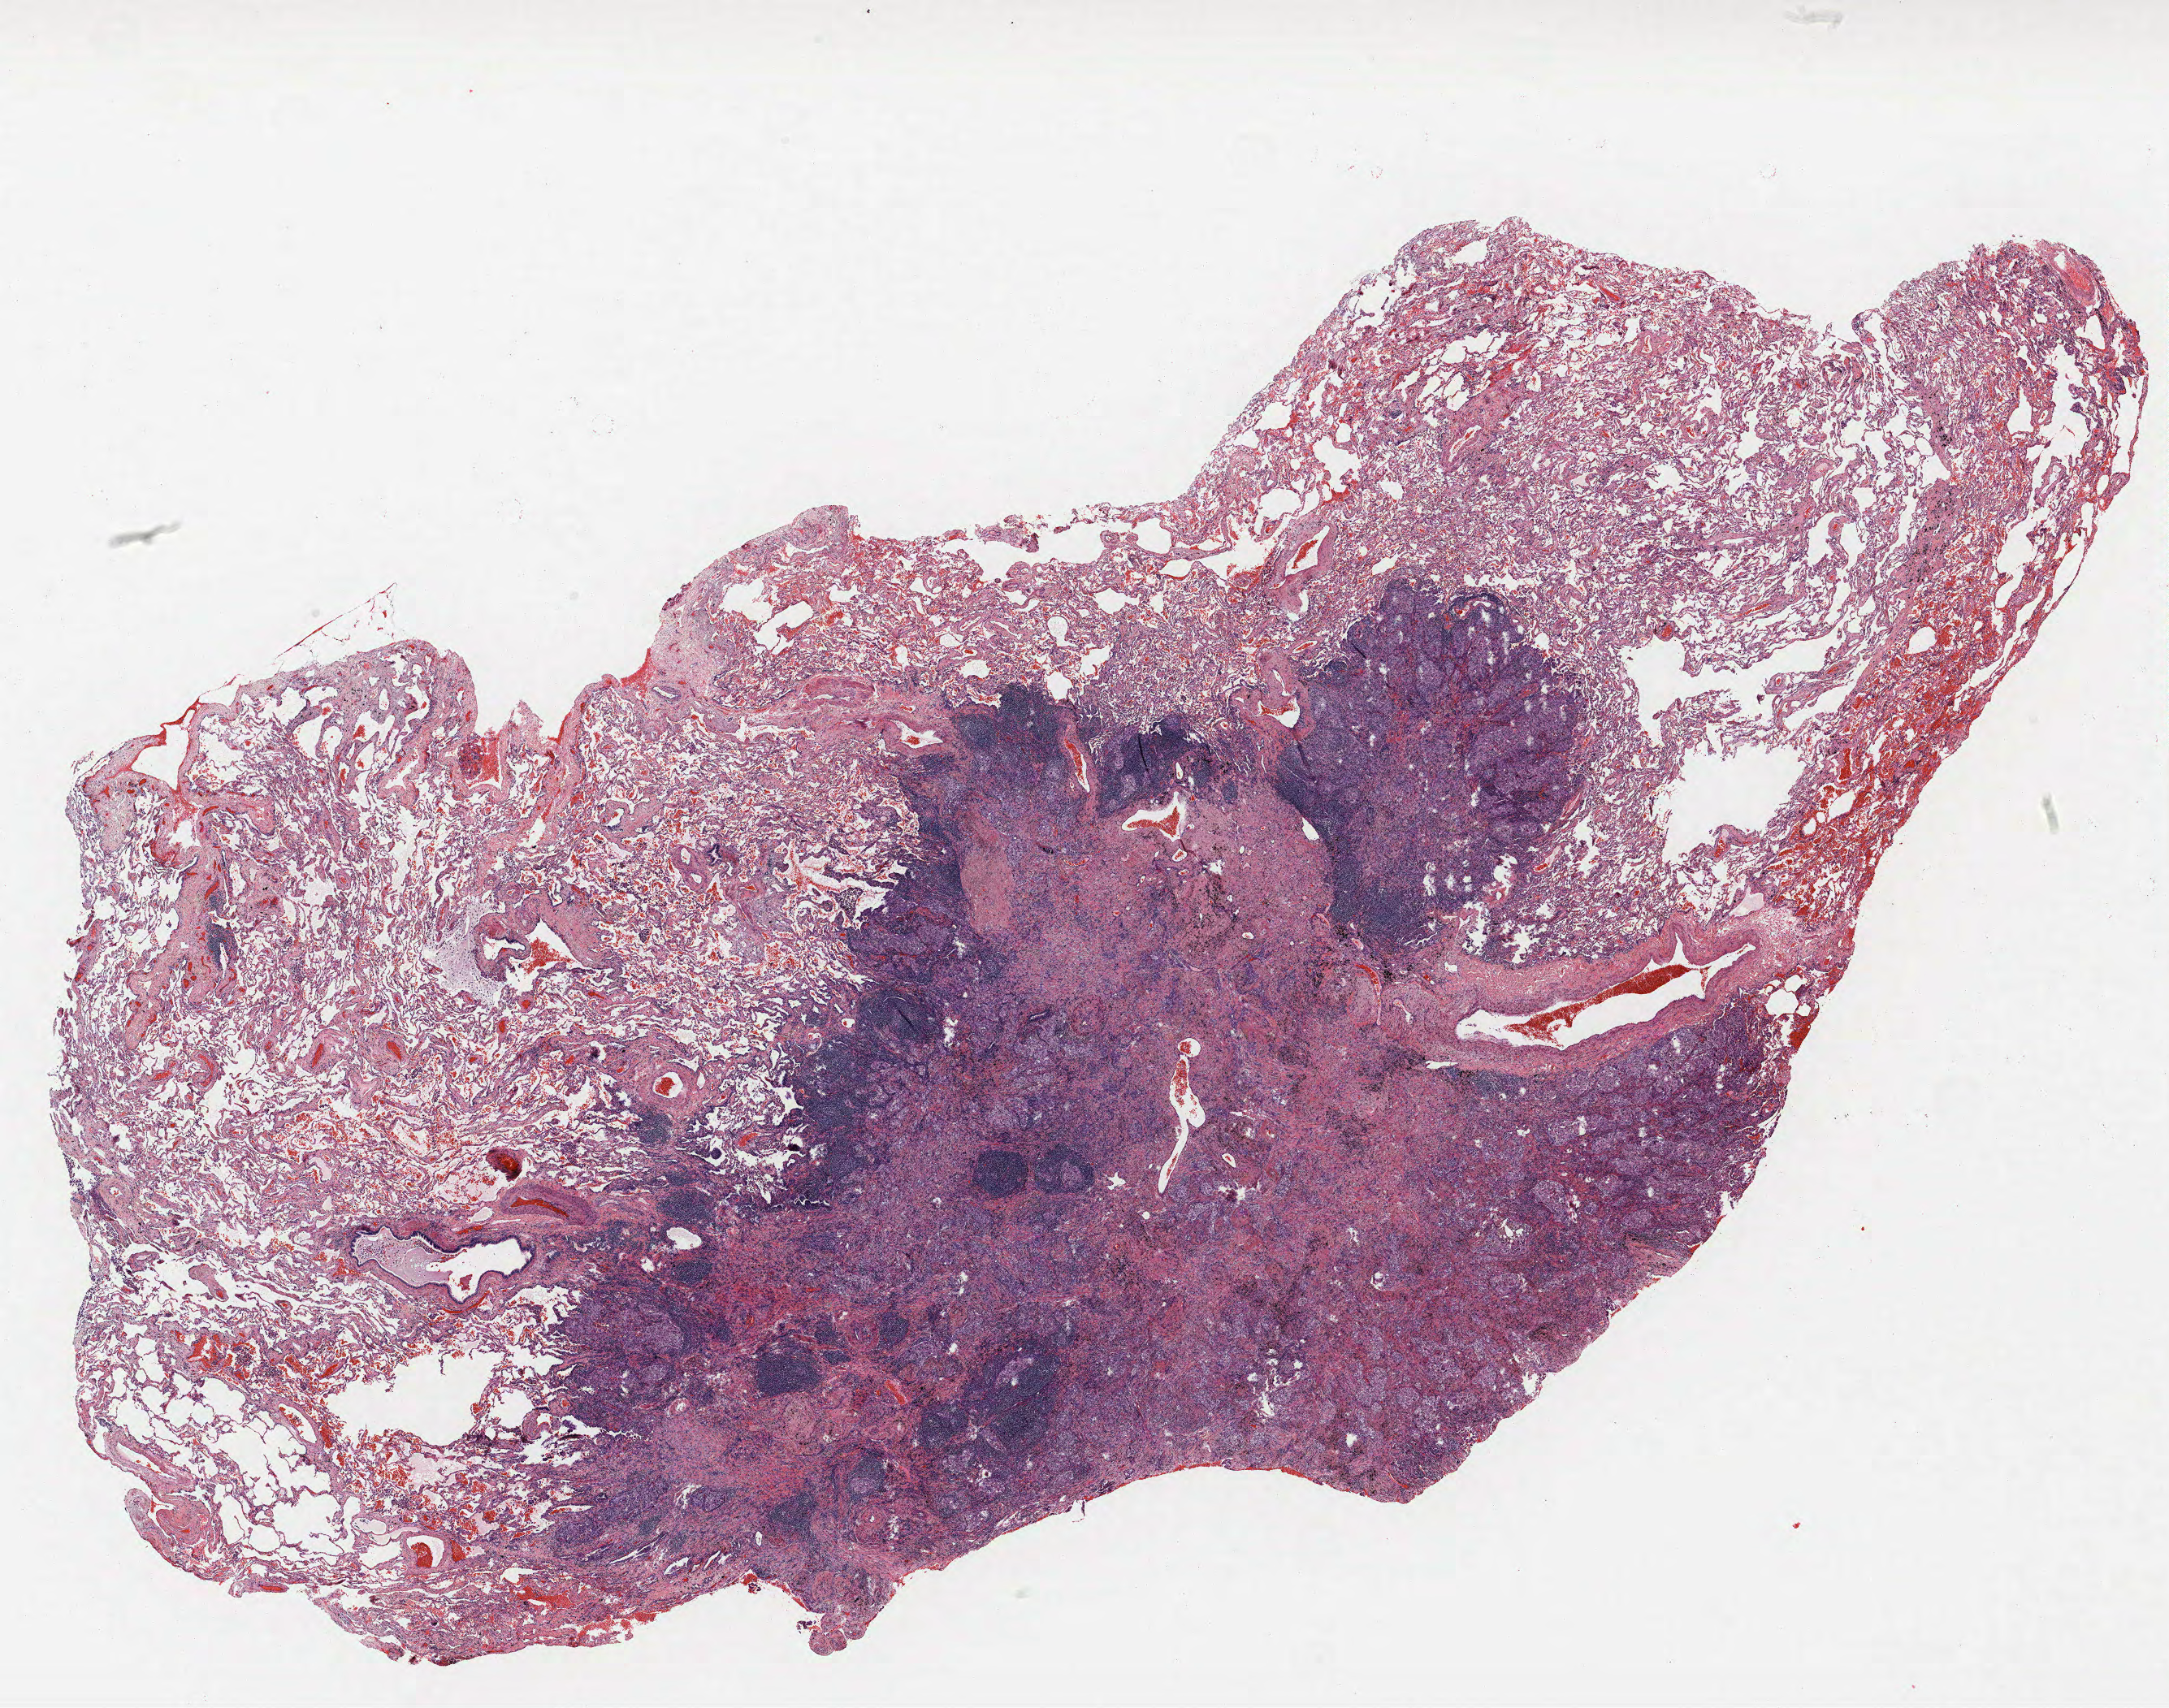
Whole-slide histology image, H&E-stained, low-resolution overview of the scanned area, about 21.4 x 16.8 mm. FFPE section. Lung tissue. Male, age 72 at enrolment. Former smoker at enrolment. Grade: moderately differentiated (G2).
Tumour size (pathology): 12 mm. Primary tumour location (clinical record): right upper lobe. Stage (AJCC 6th edition): IIA. ICD-O-3 topography: upper lobe of lung (C34.1). Participant's lung-cancer diagnosis: Adenocarcinoma, NOS.